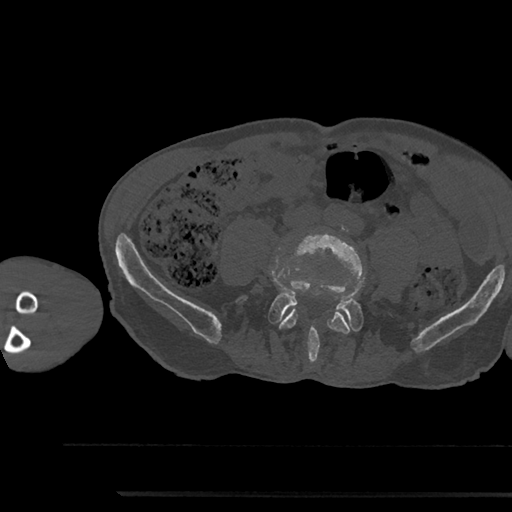
CT including the spine, one axial slice. Slice 376 of 797 in the series (ordered by position). Reconstruction kernel Br40s/3. Bone window (W 1800 / L 400 HU). 0.5 mm slice thickness. 512 × 512 image matrix, field of view 367 × 367 mm. Patient: male, 79 years. Case-level facts recorded for this patient, not image findings: primary cancer: prostate.
Annotated regions visible in this slice (semi-automatically segmented with operator editing):
- L4 vertebra: bounding box (x1, y1, x2, y2) in pixels: (279, 232, 364, 334)
- L5 vertebra: (240, 279, 362, 362)